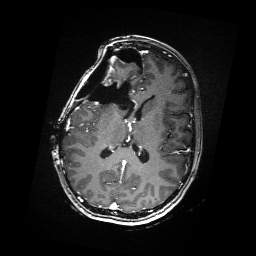
Brain MRI from a brain-tumour surgery series, one axial slice; slice 82 of 176 in the series (ordered by position); T1-weighted post-contrast; 1 mm slice thickness; 256 × 256 image matrix, field of view 256 × 256 mm. Case-level facts recorded for this patient, not image findings: histopathology: Metastatic Carcinoma from Breast primary; tumour location: Right Frontal.
Outlined on this slice (outlined manually by an expert reader):
- residual tumour: box from (x=88, y=68) to (x=117, y=103) px